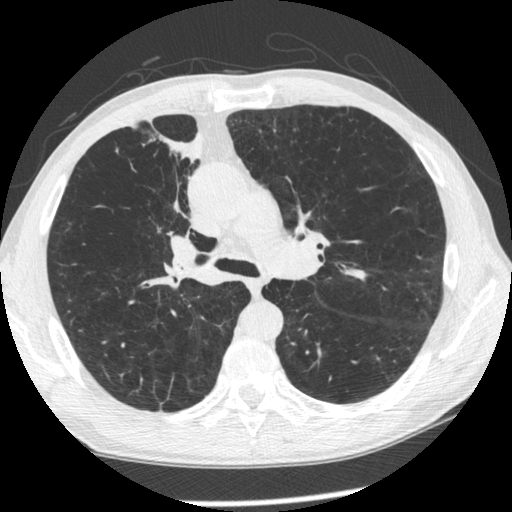
Low-dose screening chest CT, one axial slice; slice 149 of 261 in the series (ordered by position); 120 kVp; lung window (W 1500 / L -600 HU); 1.25 mm slice thickness; 512 × 512 image matrix, field of view 340 × 340 mm.
Annotated regions visible in this slice (manually delineated by an expert):
- lesion 1 (tumor, upper lobe of right lung): bounding box (x1, y1, x2, y2) in pixels: (160, 132, 205, 162)